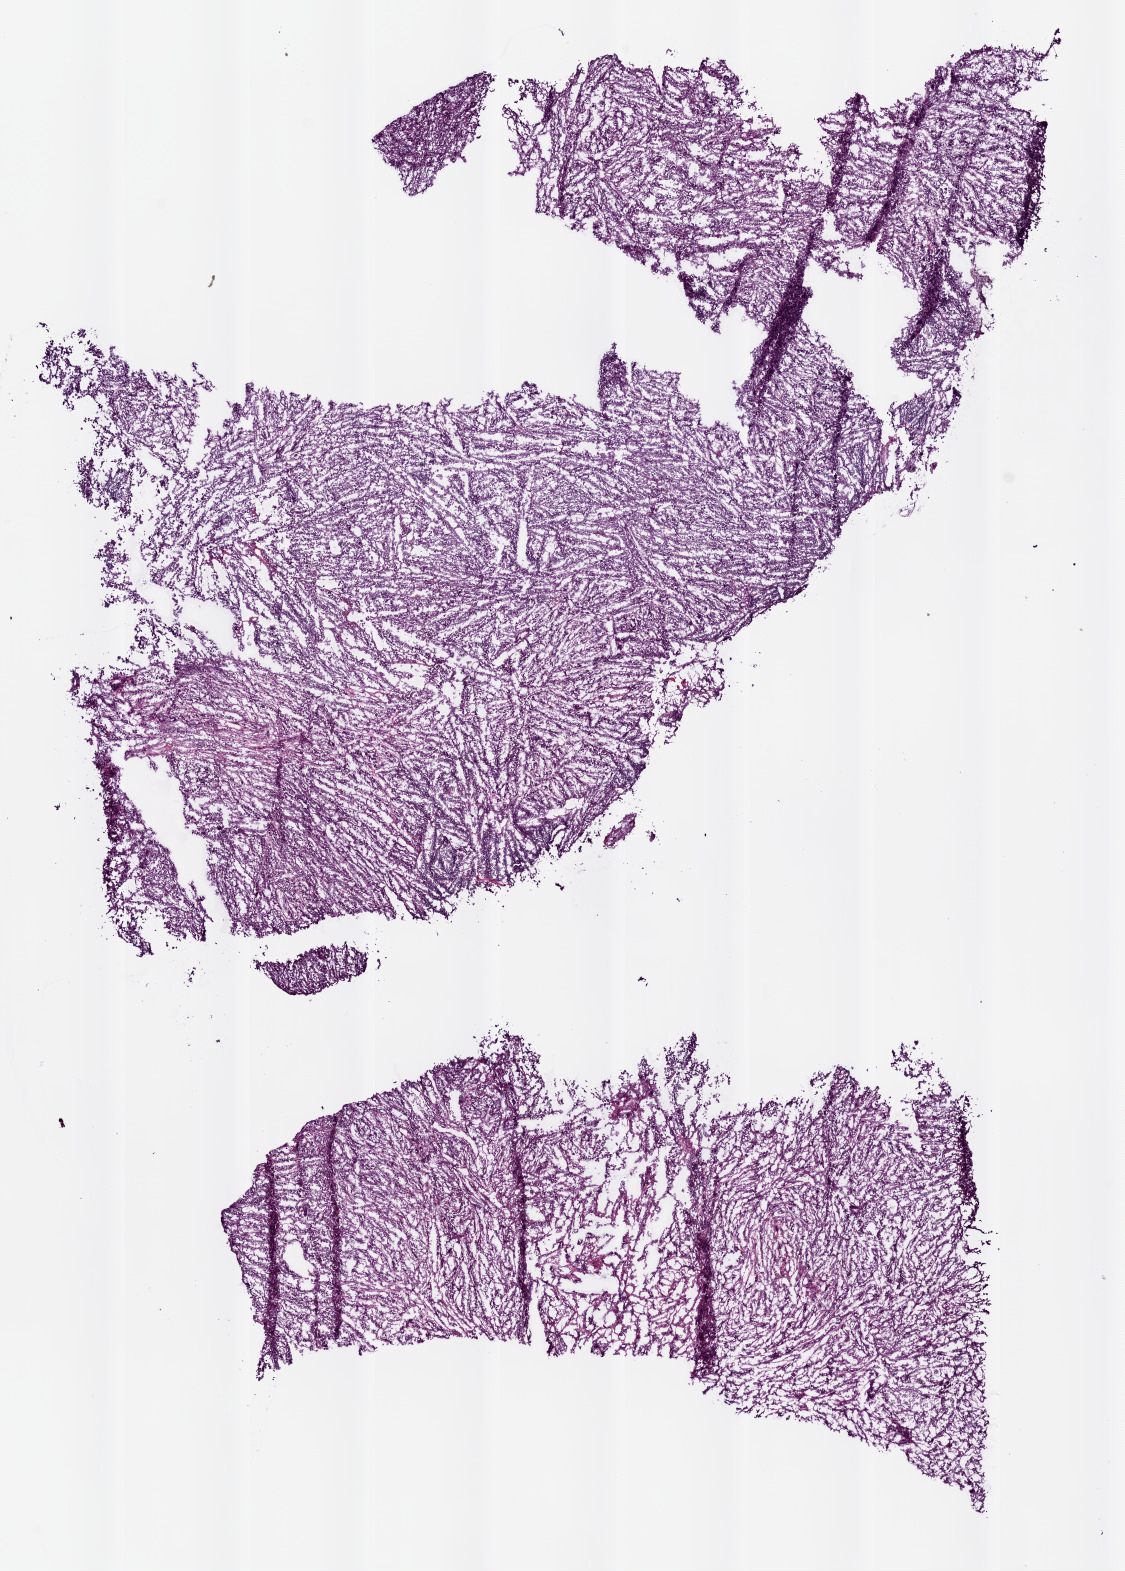
Digitized H&E tissue section (whole slide), whole scanned area (about 9.0 x 12.6 mm) shown as a low-resolution overview. Frozen section. Lung, primary tumour sample. Female patient; age at initial diagnosis 55 years. Slide review estimates, as recorded: tumour cells 90%, tumour nuclei 75%, normal cells 0%, stromal cells 10%, necrosis 1%. Inflammatory infiltration, as recorded: lymphocyte infiltration 15%, monocyte infiltration 5%, neutrophil infiltration 0%.
* diagnosis: Adenocarcinoma with mixed subtypes (upper lobe, lung)
* AJCC pathologic stage: IB (6th edition)